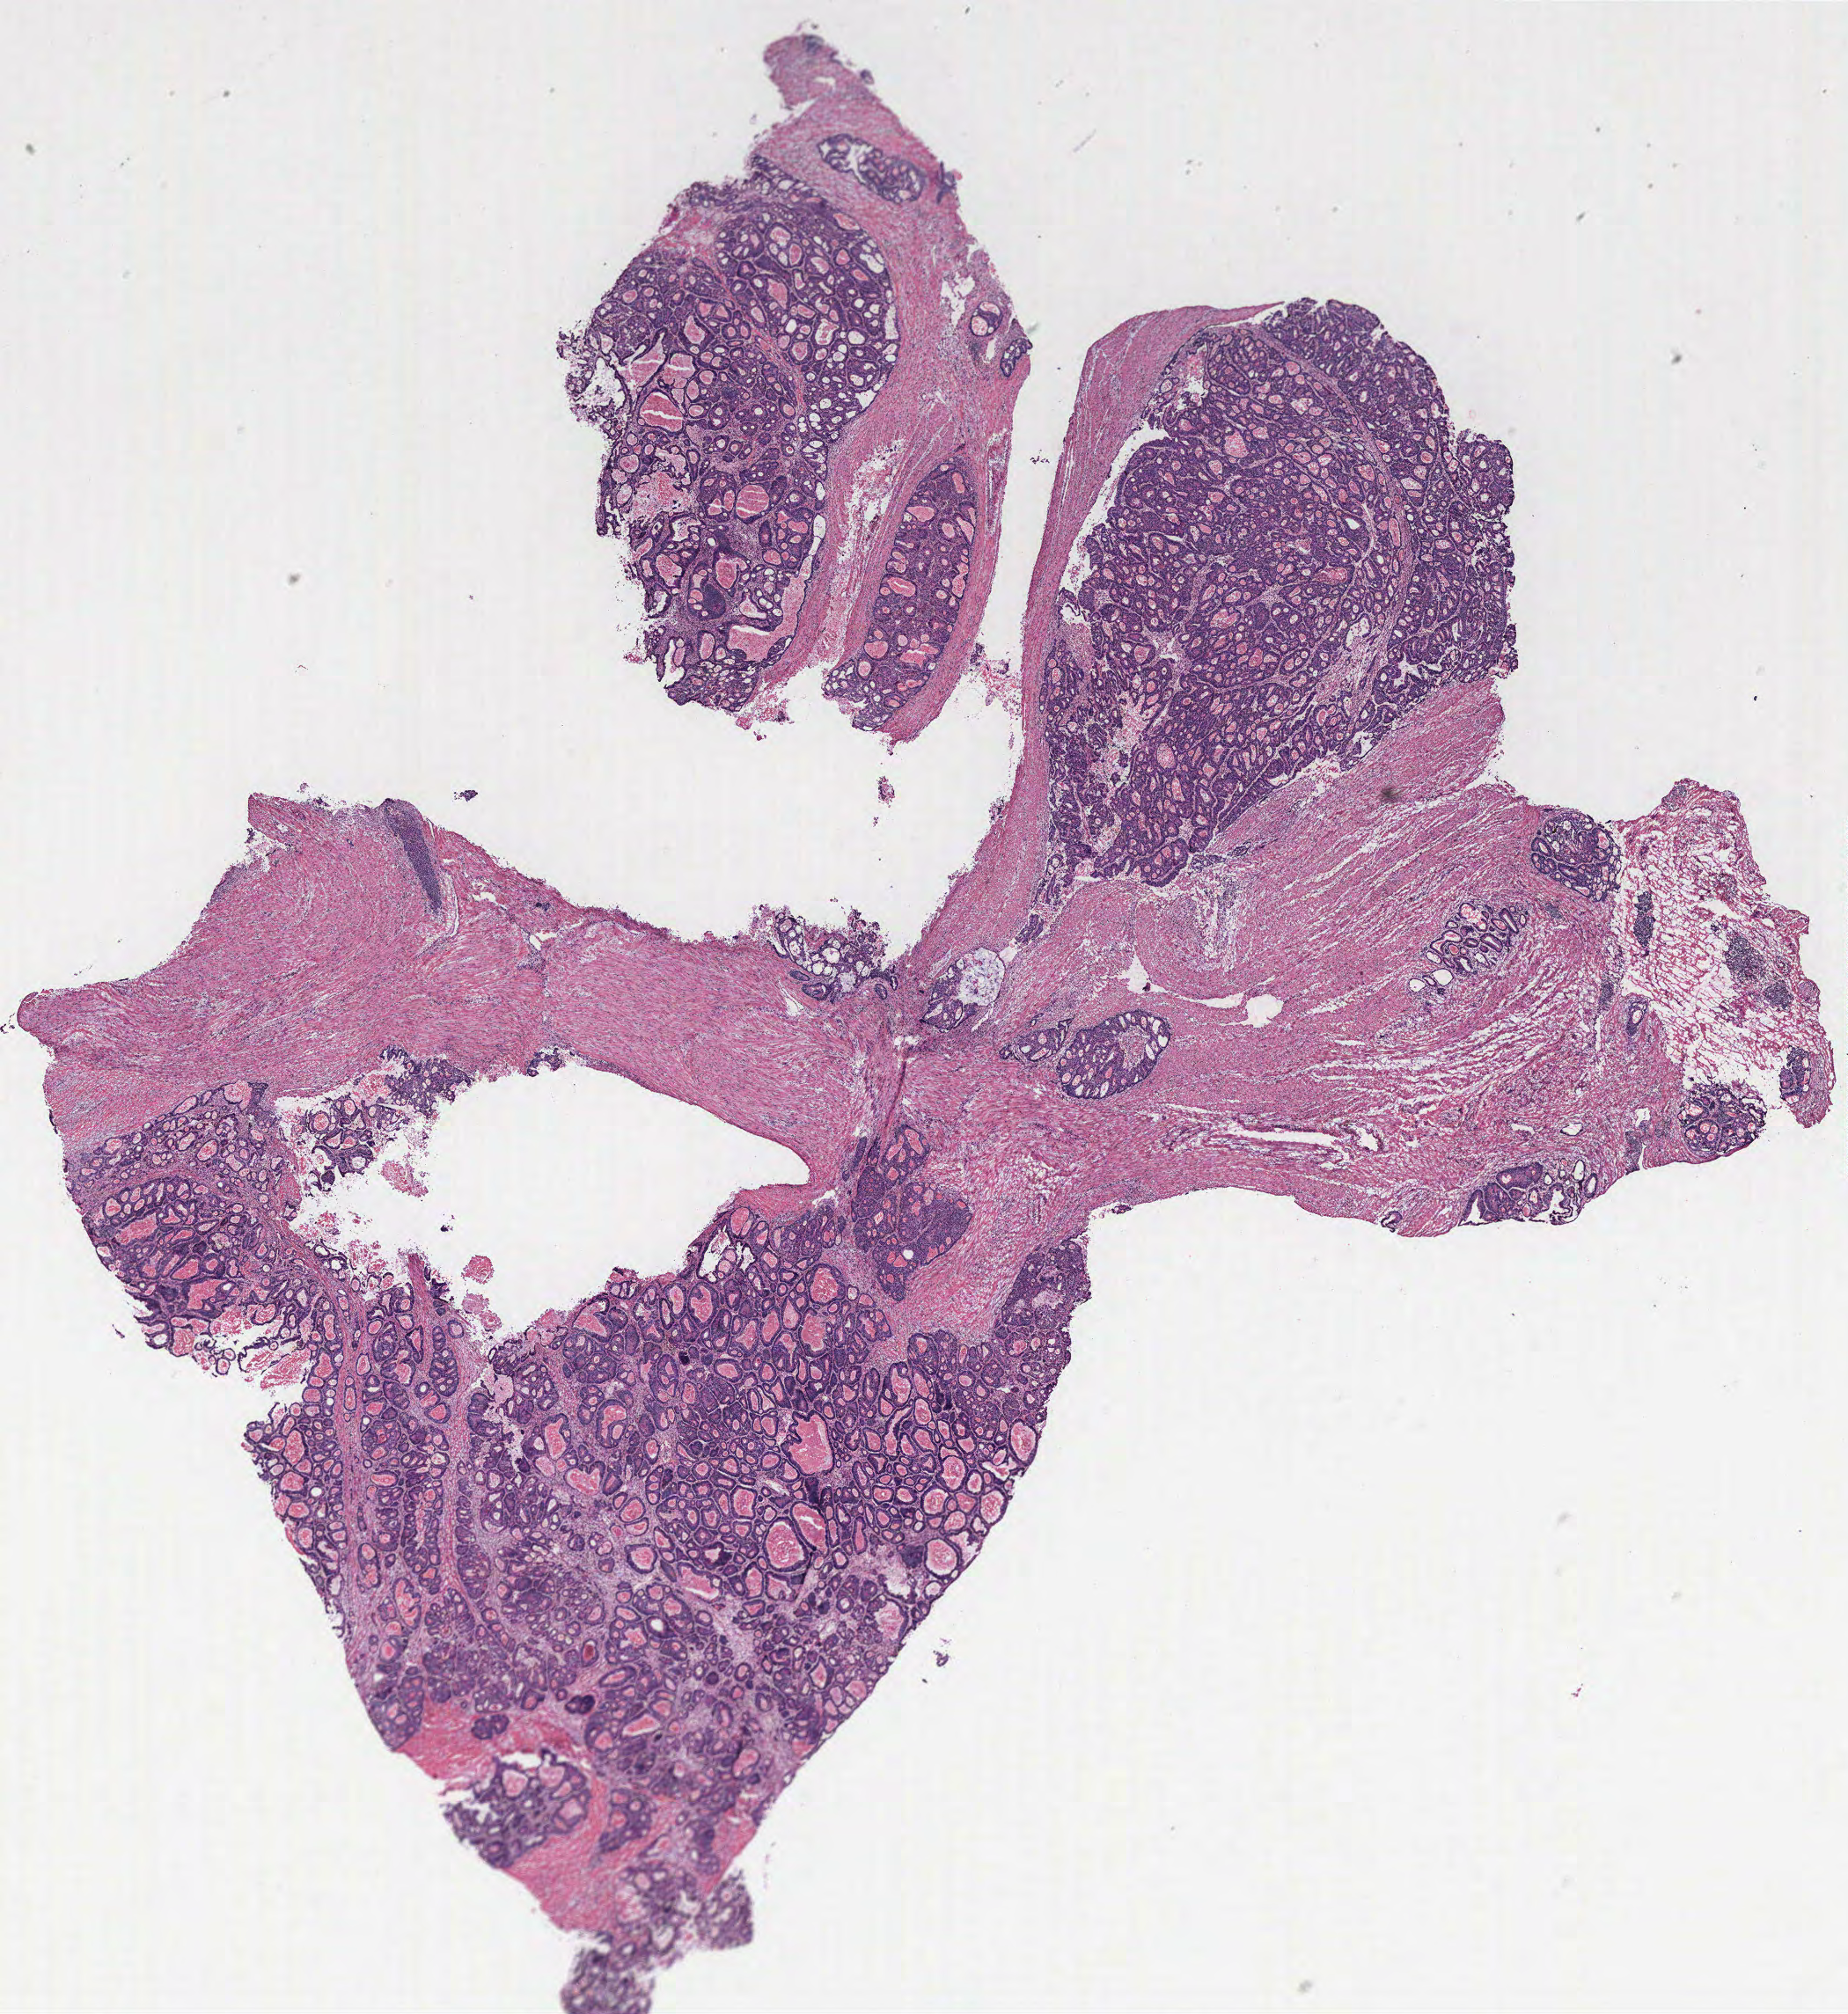
H&E-stained whole-slide image — low-resolution overview of the scanned area, about 16.8 x 18.3 mm. Tumour tissue sample, colon. Patient: male, age 67 years.
AJCC pathologic stage: IIIB. Primary tumour site (as recorded): colon. Histologic diagnosis: Adenocarcinoma, NOS.